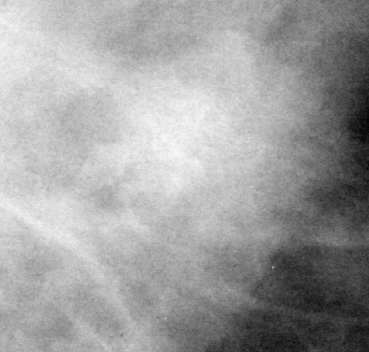
Cropped region of a digitized screen-film mammogram centred on a radiologist-marked abnormality, left breast, MLO view.
- Mass, shape lobulated, margins microlobulated; BI-RADS assessment category 4; pathology (as recorded): malignant.